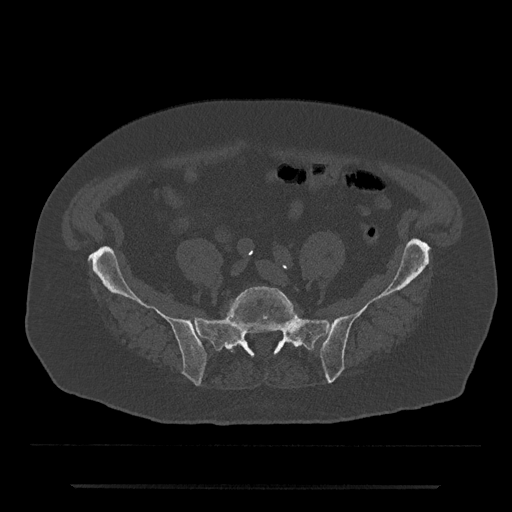
CT including the spine, one axial slice. Position 254 of 797 along the scan axis. Reconstruction kernel Br40s/3. 120 kVp. Bone window (W 1800 / L 400 HU). 512 × 512 image matrix, field of view 434 × 434 mm. Patient: male, 80 years. From the clinical record (not read from this slice): primary cancer: prostate.
Outlined on this slice (semi-automatic segmentation, software-assisted and operator-edited):
- L5 vertebra: bounding box [x1, y1, x2, y2] px = [226, 286, 297, 352]